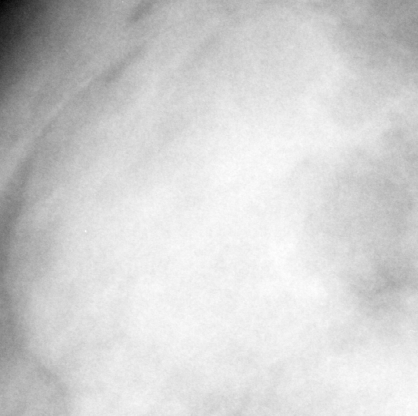
Region of interest cut from a scanned film mammogram (one marked finding), right breast, CC view.
Mass, shape oval, margins obscured; BI-RADS assessment category 3; subtlety rating 4 on a 1 (subtle) to 5 (obvious) scale; pathology (as recorded): benign.